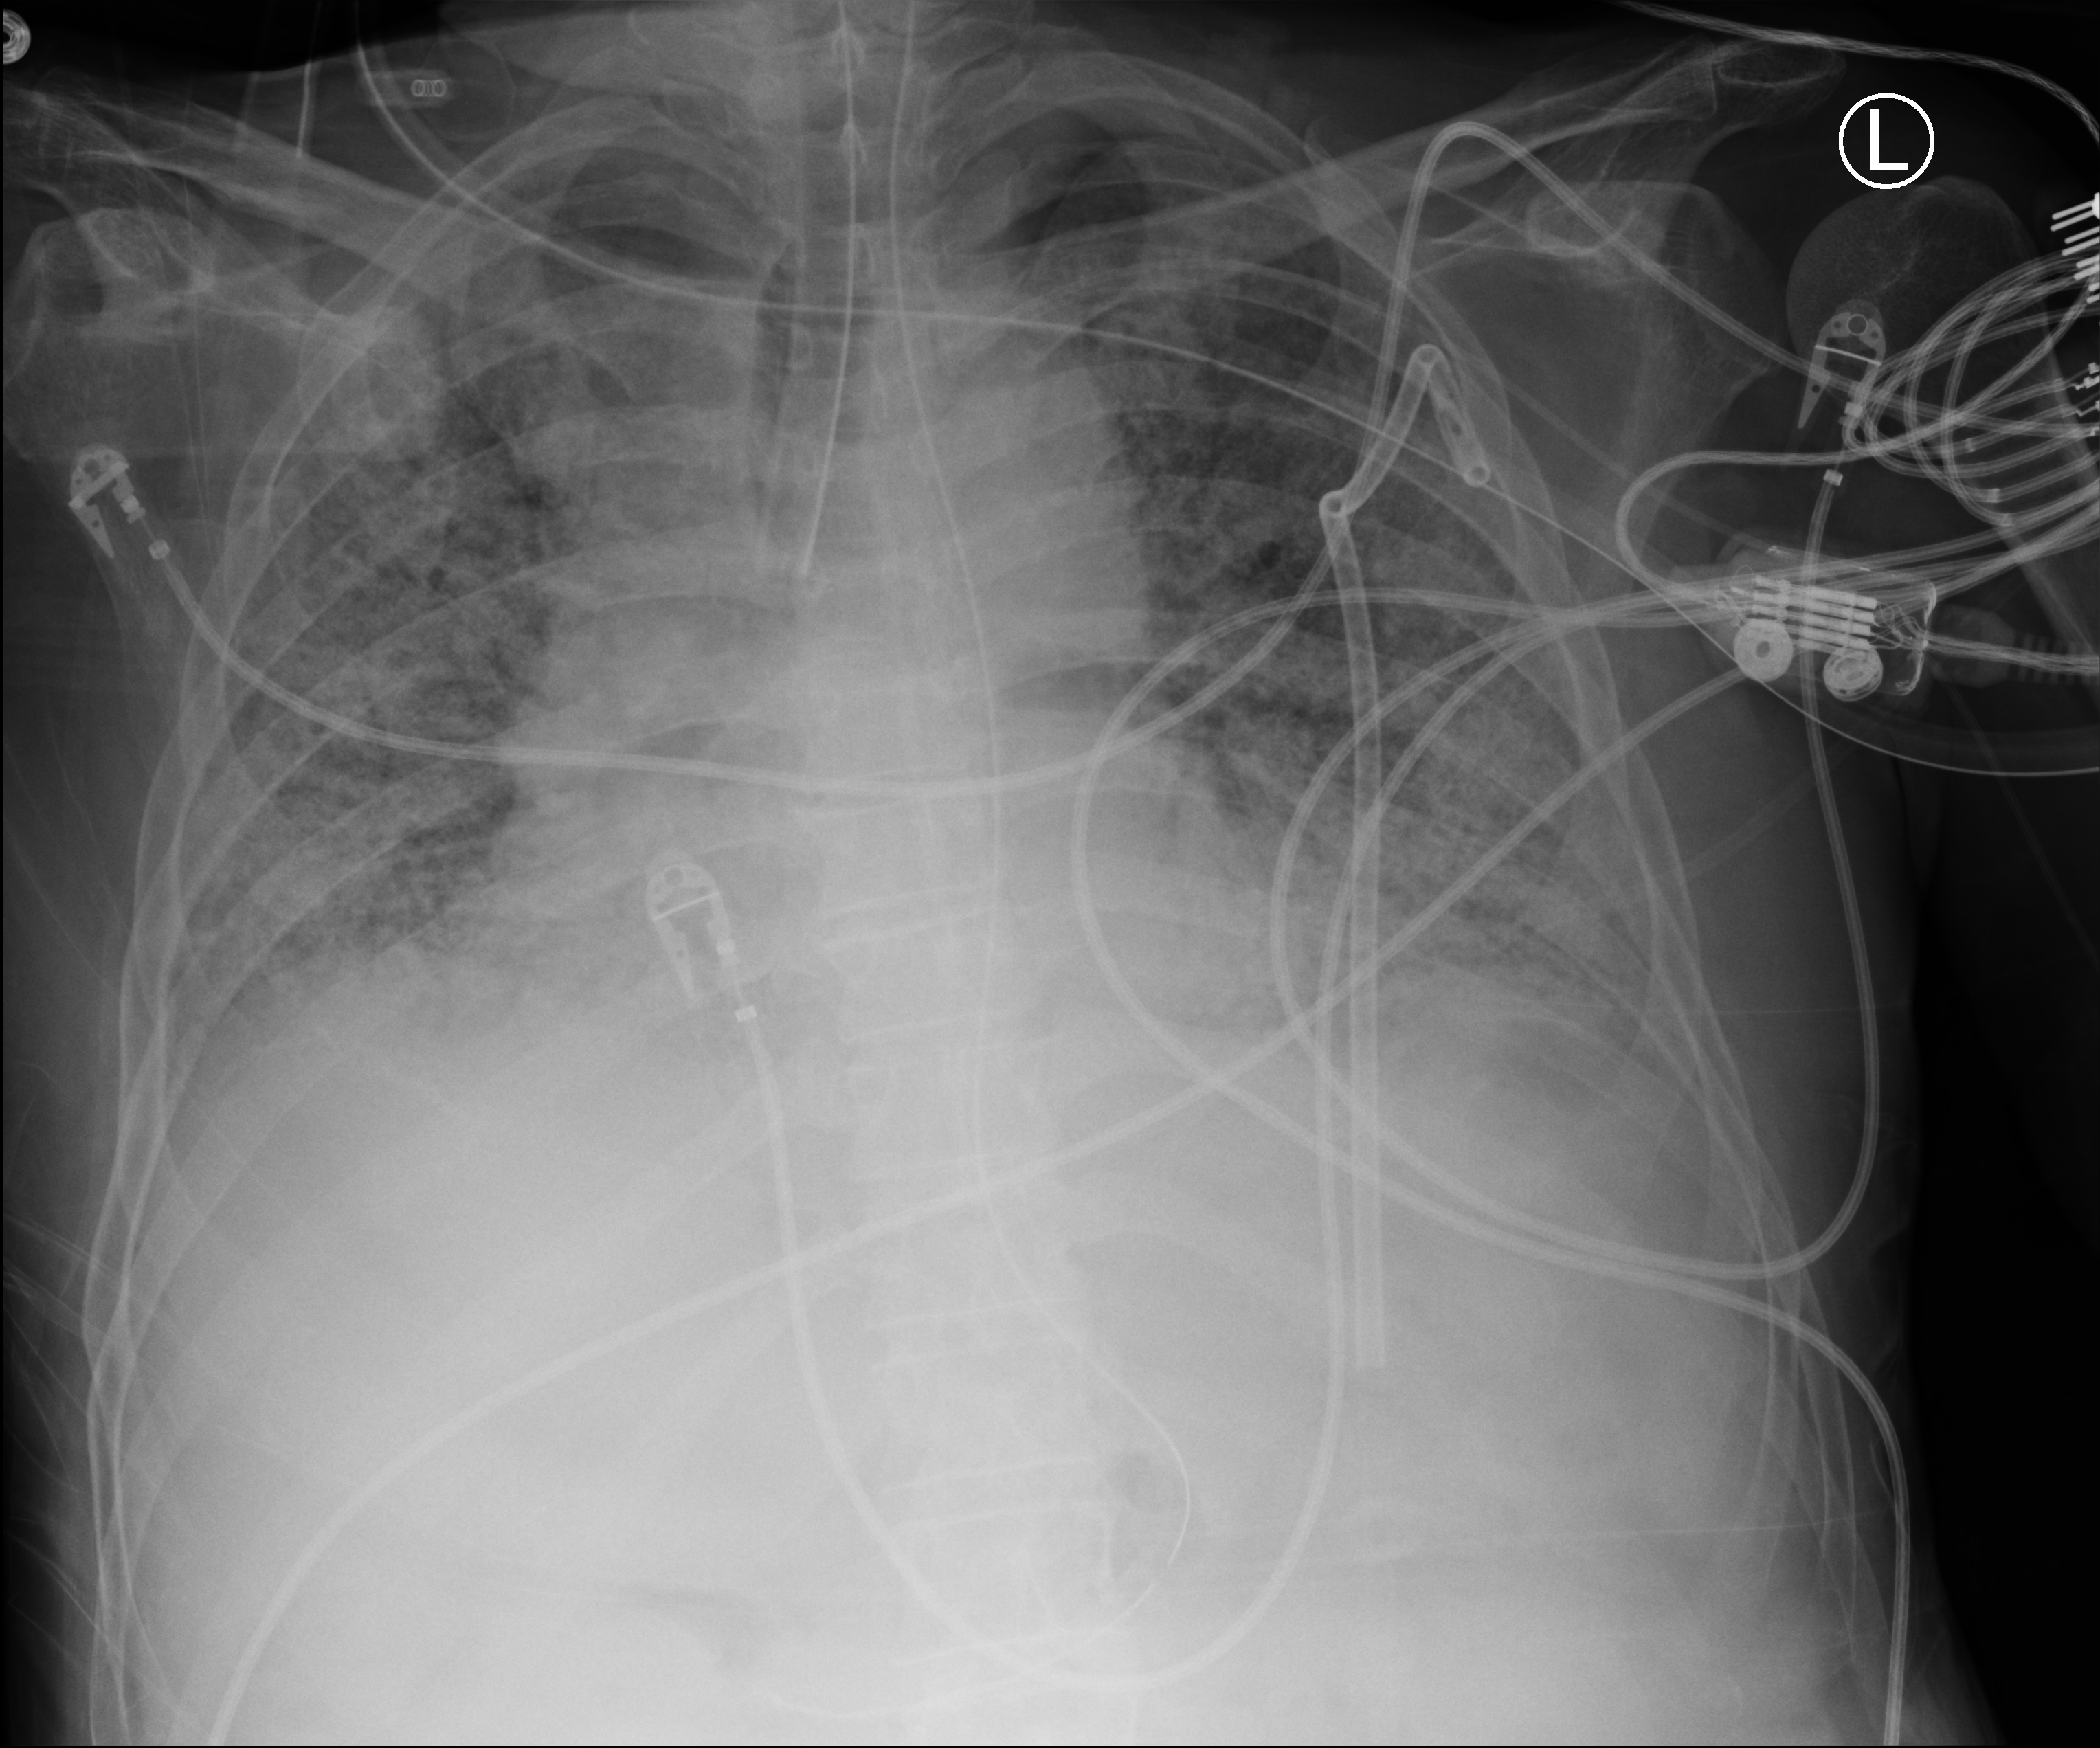
Bedside chest radiograph (computed radiography), anteroposterior (AP) projection. Male patient hospitalised with COVID-19, age 60–74 years.
From the hospital-stay record, not from the radiograph (when in the stay this image was taken is not recorded): mechanically ventilated during this hospital stay: yes.